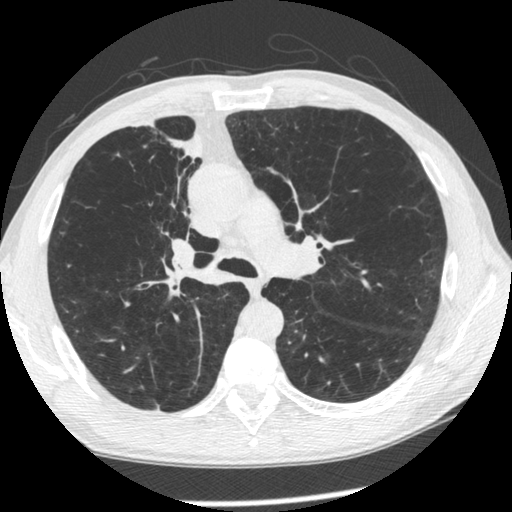
Low-dose screening chest CT, one axial slice; slice 151 of 261 in the series (ordered by position); reconstruction kernel STANDARD; 120 kVp; lung window (W 1500 / L -600 HU); 512 × 512 image matrix, field of view 340 × 340 mm.
Annotated regions visible in this slice (outlined manually by an expert reader):
- lesion 1 (tumor, upper lobe of right lung): bounding box <169,133,204,160> (left, top, right, bottom; pixels)